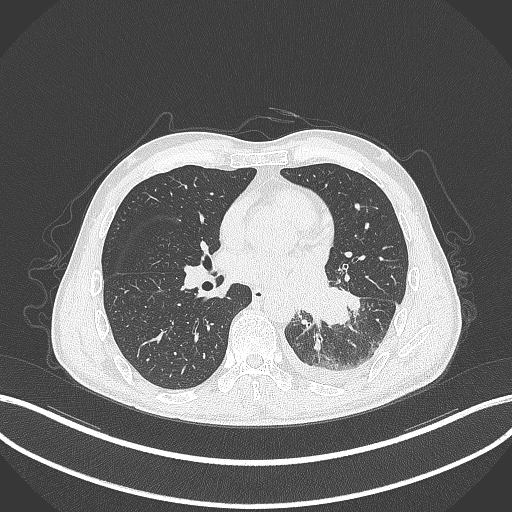
Chest CT, one axial slice; slice 145 of 295 in the series (ordered by position); reconstruction kernel B70f; 120 kVp; lung window (W 1500 / L -600 HU); 1 mm slice thickness; 512 × 512 image matrix. Male patient, age 47 years. From the clinical record (not read from this slice): clinical TNM (as recorded): T3 N1 M1c.
Structures marked on this image (bounding box drawn by a radiologist):
- lung tumour (recorded histology: small cell carcinoma): bounding box [x1, y1, x2, y2] px = [308, 284, 351, 328]